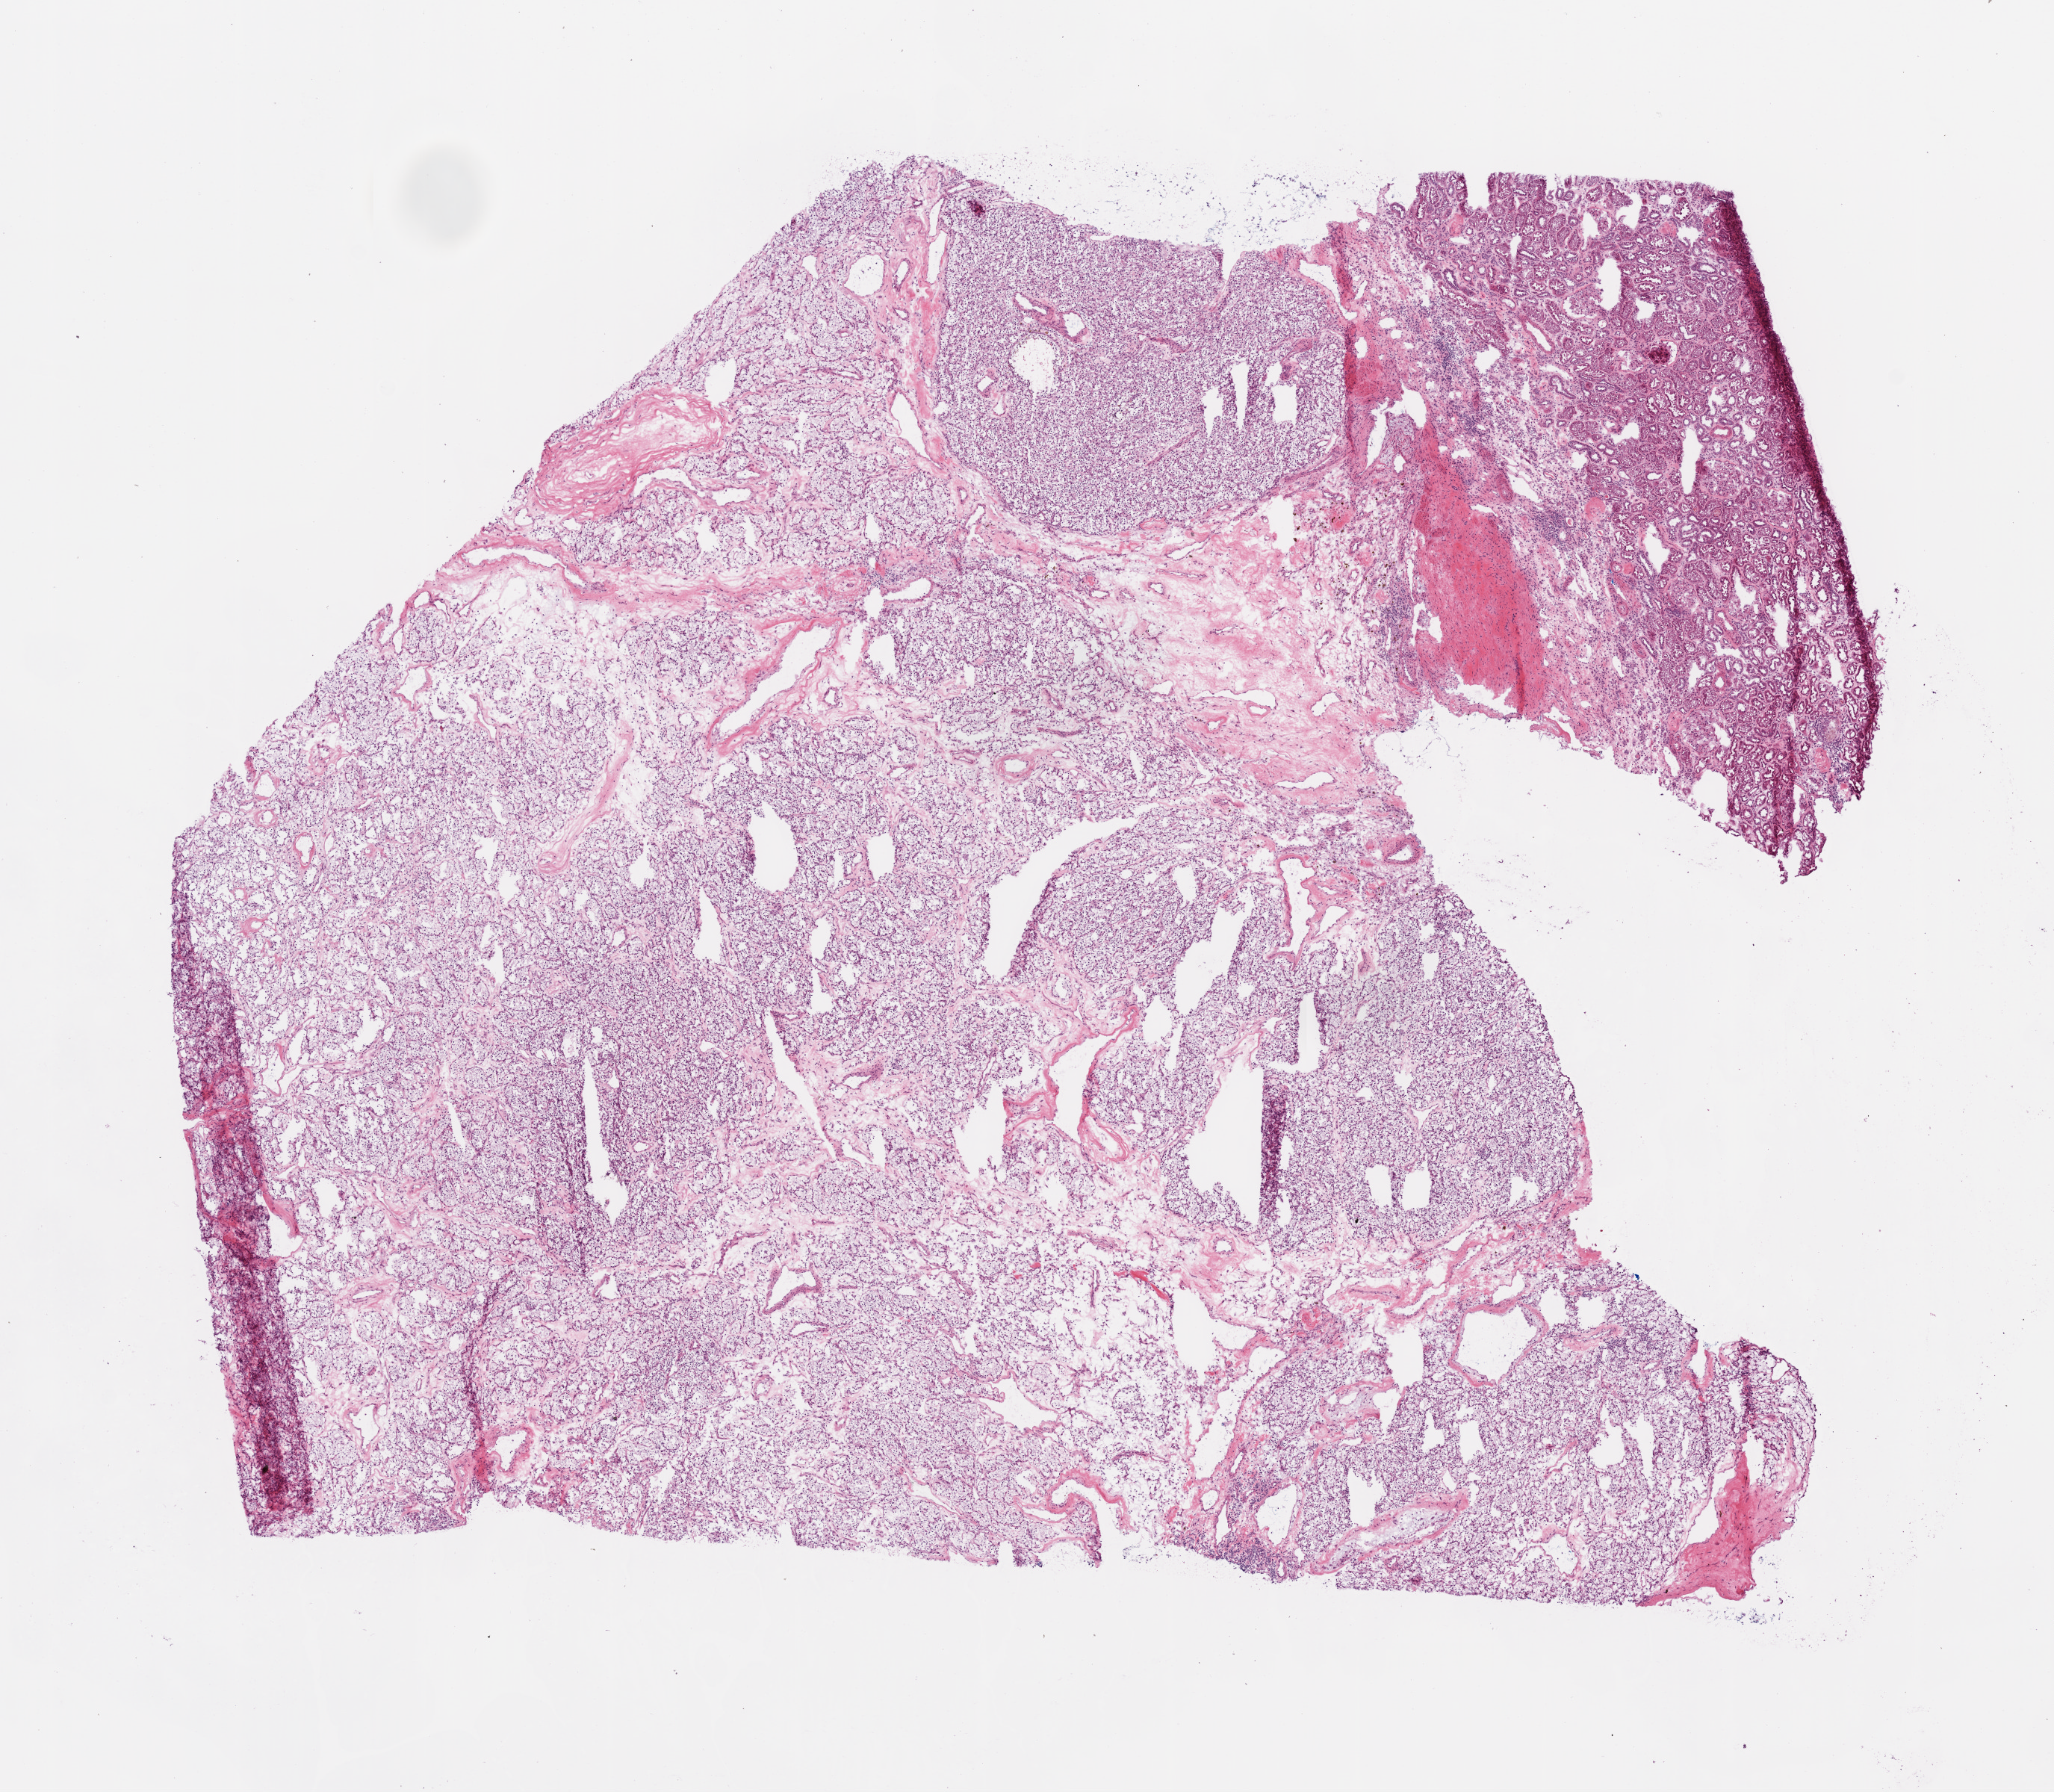
Digitized H&E tissue section (whole slide) — low-resolution overview of the scanned area, about 11.0 x 9.6 mm, frozen section from the bottom of the tissue portion, sample: primary tumour, kidney. Patient: male, age at initial diagnosis 43 years. Histologic grade: G2 (moderately differentiated). Composition of this section per pathologist review: tumour cells 75%, tumour nuclei 80%, normal cells 15%, stromal cells 10%, necrosis 0%.
Histologic diagnosis: Clear cell adenocarcinoma, NOS. AJCC pathologic stage: I (7th edition).